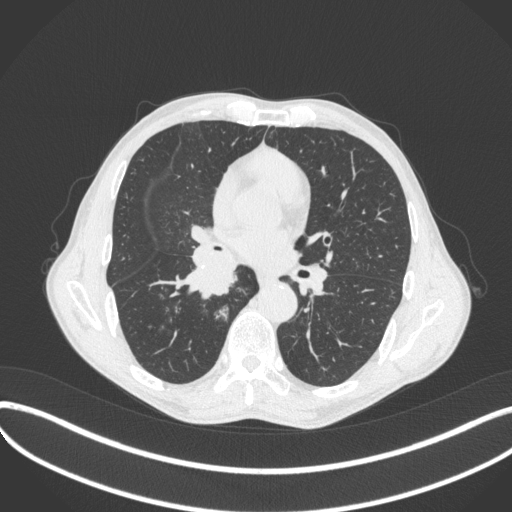
Chest CT, one axial slice. Position 222 of 481 along the scan axis. Reconstruction kernel B31f. 120 kVp. Lung window (W 1500 / L -600 HU). 1 mm slice thickness. 512 × 512 image matrix, field of view 400 × 400 mm. Patient: male, 65 years. Case-level facts recorded for this patient, not image findings: clinical TNM (as recorded): T2a N0 M0; histopathological grade: G2.
Outlined on this slice (rectangle marked by the reading radiologist):
- lung tumour (recorded histology: squamous cell carcinoma): bounding box <178,242,243,300> (left, top, right, bottom; pixels)